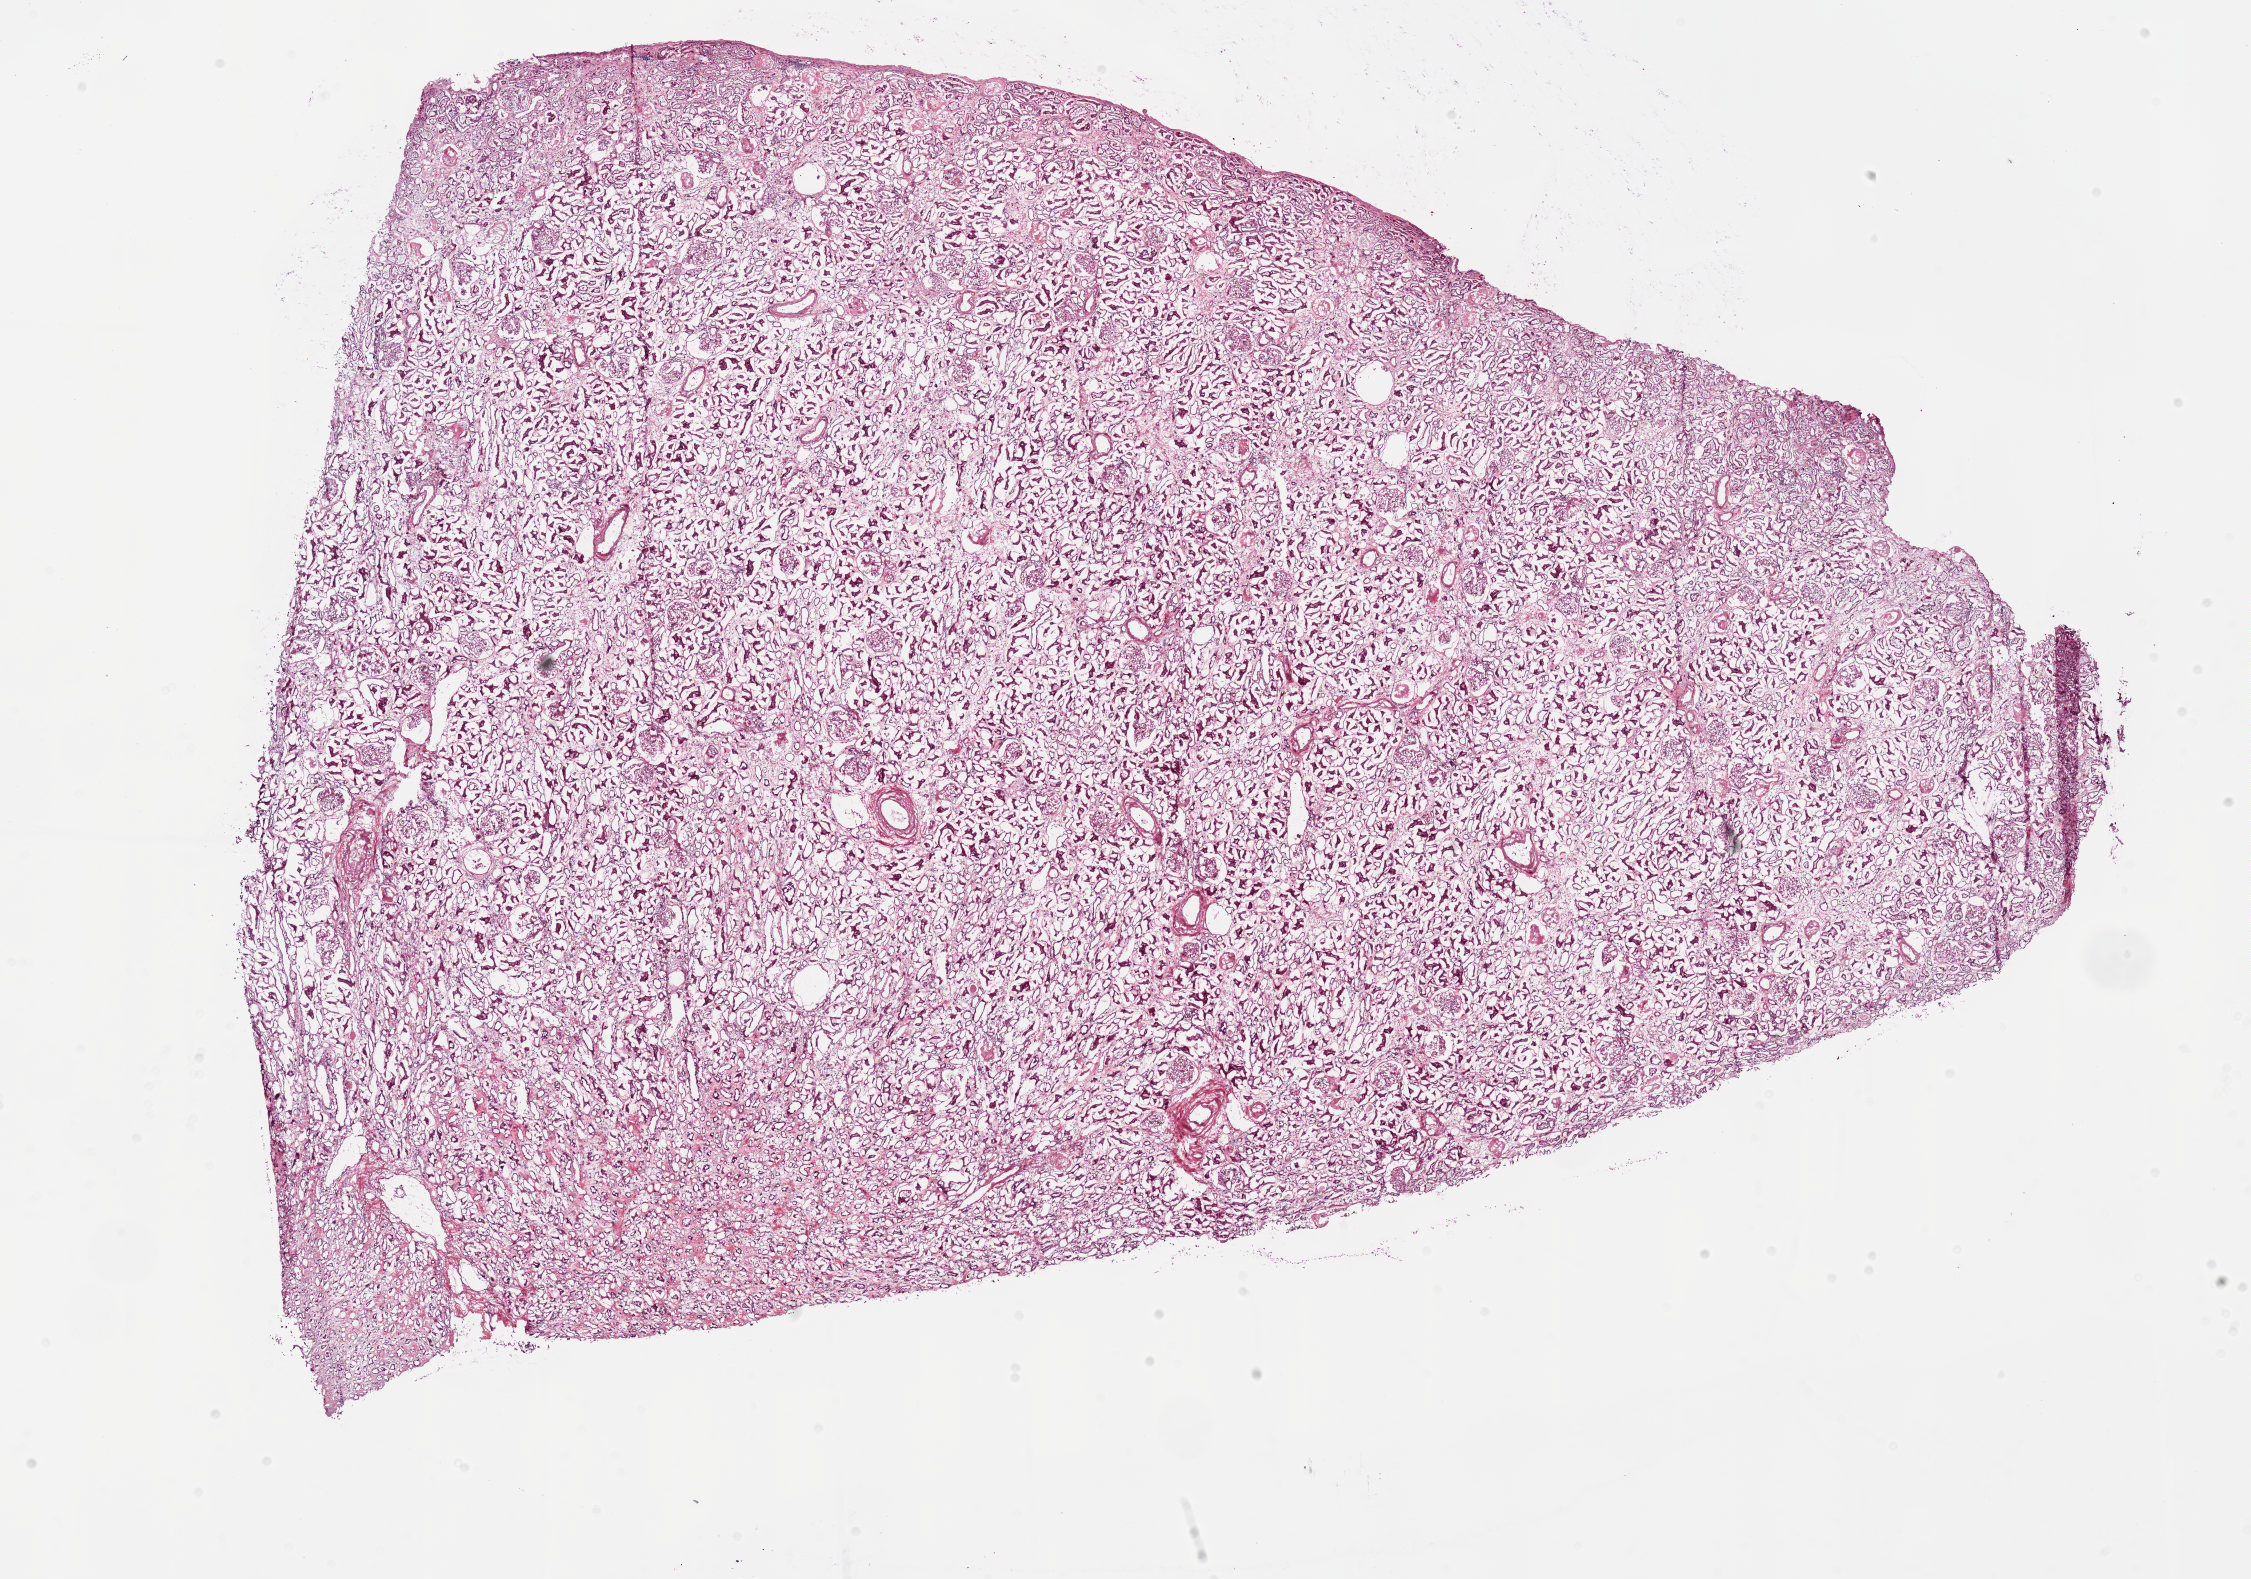
H&E whole-slide image, a low-resolution overview of the entire scanned area, about 17.9 x 12.5 mm (acquisition: 20x scan), frozen section from the bottom of the tissue portion, sample: solid tissue normal (non-tumour tissue), kidney. Male, age 81 years at initial diagnosis.
* this section: solid tissue normal (non-tumour) sample from the same patient
* patient diagnosis: Clear cell adenocarcinoma, NOS